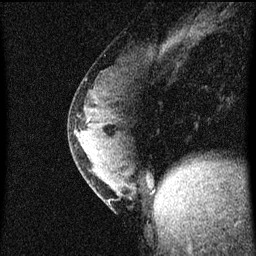
Breast MRI (dynamic contrast-enhanced), one sagittal slice; slice 25 of 60 in the series (ordered by position); dynamic contrast-enhanced series, image 2 of 4 at this slice position (ordered by acquisition); 1.5 T; TE 4.2 ms, TR 8 ms; 2 mm slice thickness; 256 × 256 image matrix, field of view 180 × 180 mm. Female patient, age 33 years.
Annotated regions visible in this slice (semi-automatically segmented with operator editing):
- analysis volume of interest (the breast-tissue region the enhancement analysis was run in; not a lesion): bounding box (x1, y1, x2, y2) in pixels: (69, 76, 146, 211)
- tumour enhancement mask (voxels above the 70 % enhancement threshold inside the analysis volume of interest): (79, 120, 89, 151)